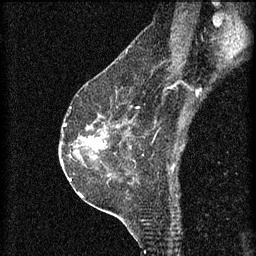
Breast MRI (dynamic contrast-enhanced), one sagittal slice. Position 39 of 60 along the scan axis. 3 images stored at this slice position (order not interpretable as contrast timing). 1.5 T. TE 4.2 ms, TR 8.2 ms. 2 mm slice thickness. 256 × 256 image matrix, field of view 180 × 180 mm. Patient: female, 60 years.
Annotated regions visible in this slice (semi-automatically segmented with operator editing):
- analysis volume of interest (the breast-tissue region the enhancement analysis was run in; not a lesion): box from (x=74, y=124) to (x=111, y=159) px
- tumour enhancement mask (voxels above the 70 % enhancement threshold inside the analysis volume of interest): (x=86, y=136)–(x=105, y=151)